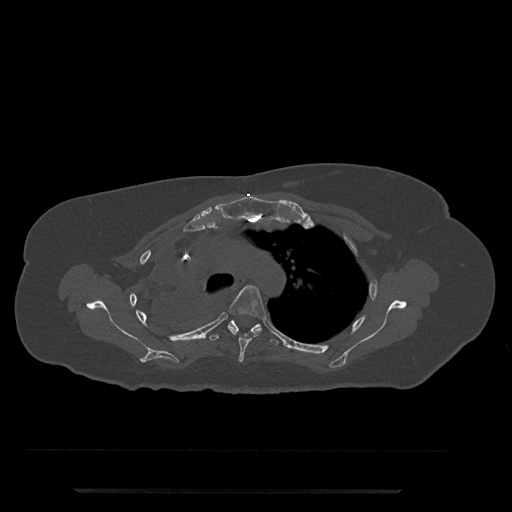
CT including the spine, one axial slice. Slice 572 of 797 in the series (ordered by position). 120 kVp. Bone window (W 1800 / L 400 HU). 0.5 mm slice thickness. 512 × 512 image matrix, field of view 440 × 440 mm. Patient: female, 51 years. From the clinical record (not read from this slice): primary cancer: neuro; vertebrae with lytic lesions (as recorded): T8.
Structures marked on this image (semi-automatic segmentation, software-assisted and operator-edited):
- T4 vertebra: bounding box (x1, y1, x2, y2) in pixels: (229, 285, 266, 362)
- T5 vertebra: (209, 320, 283, 346)